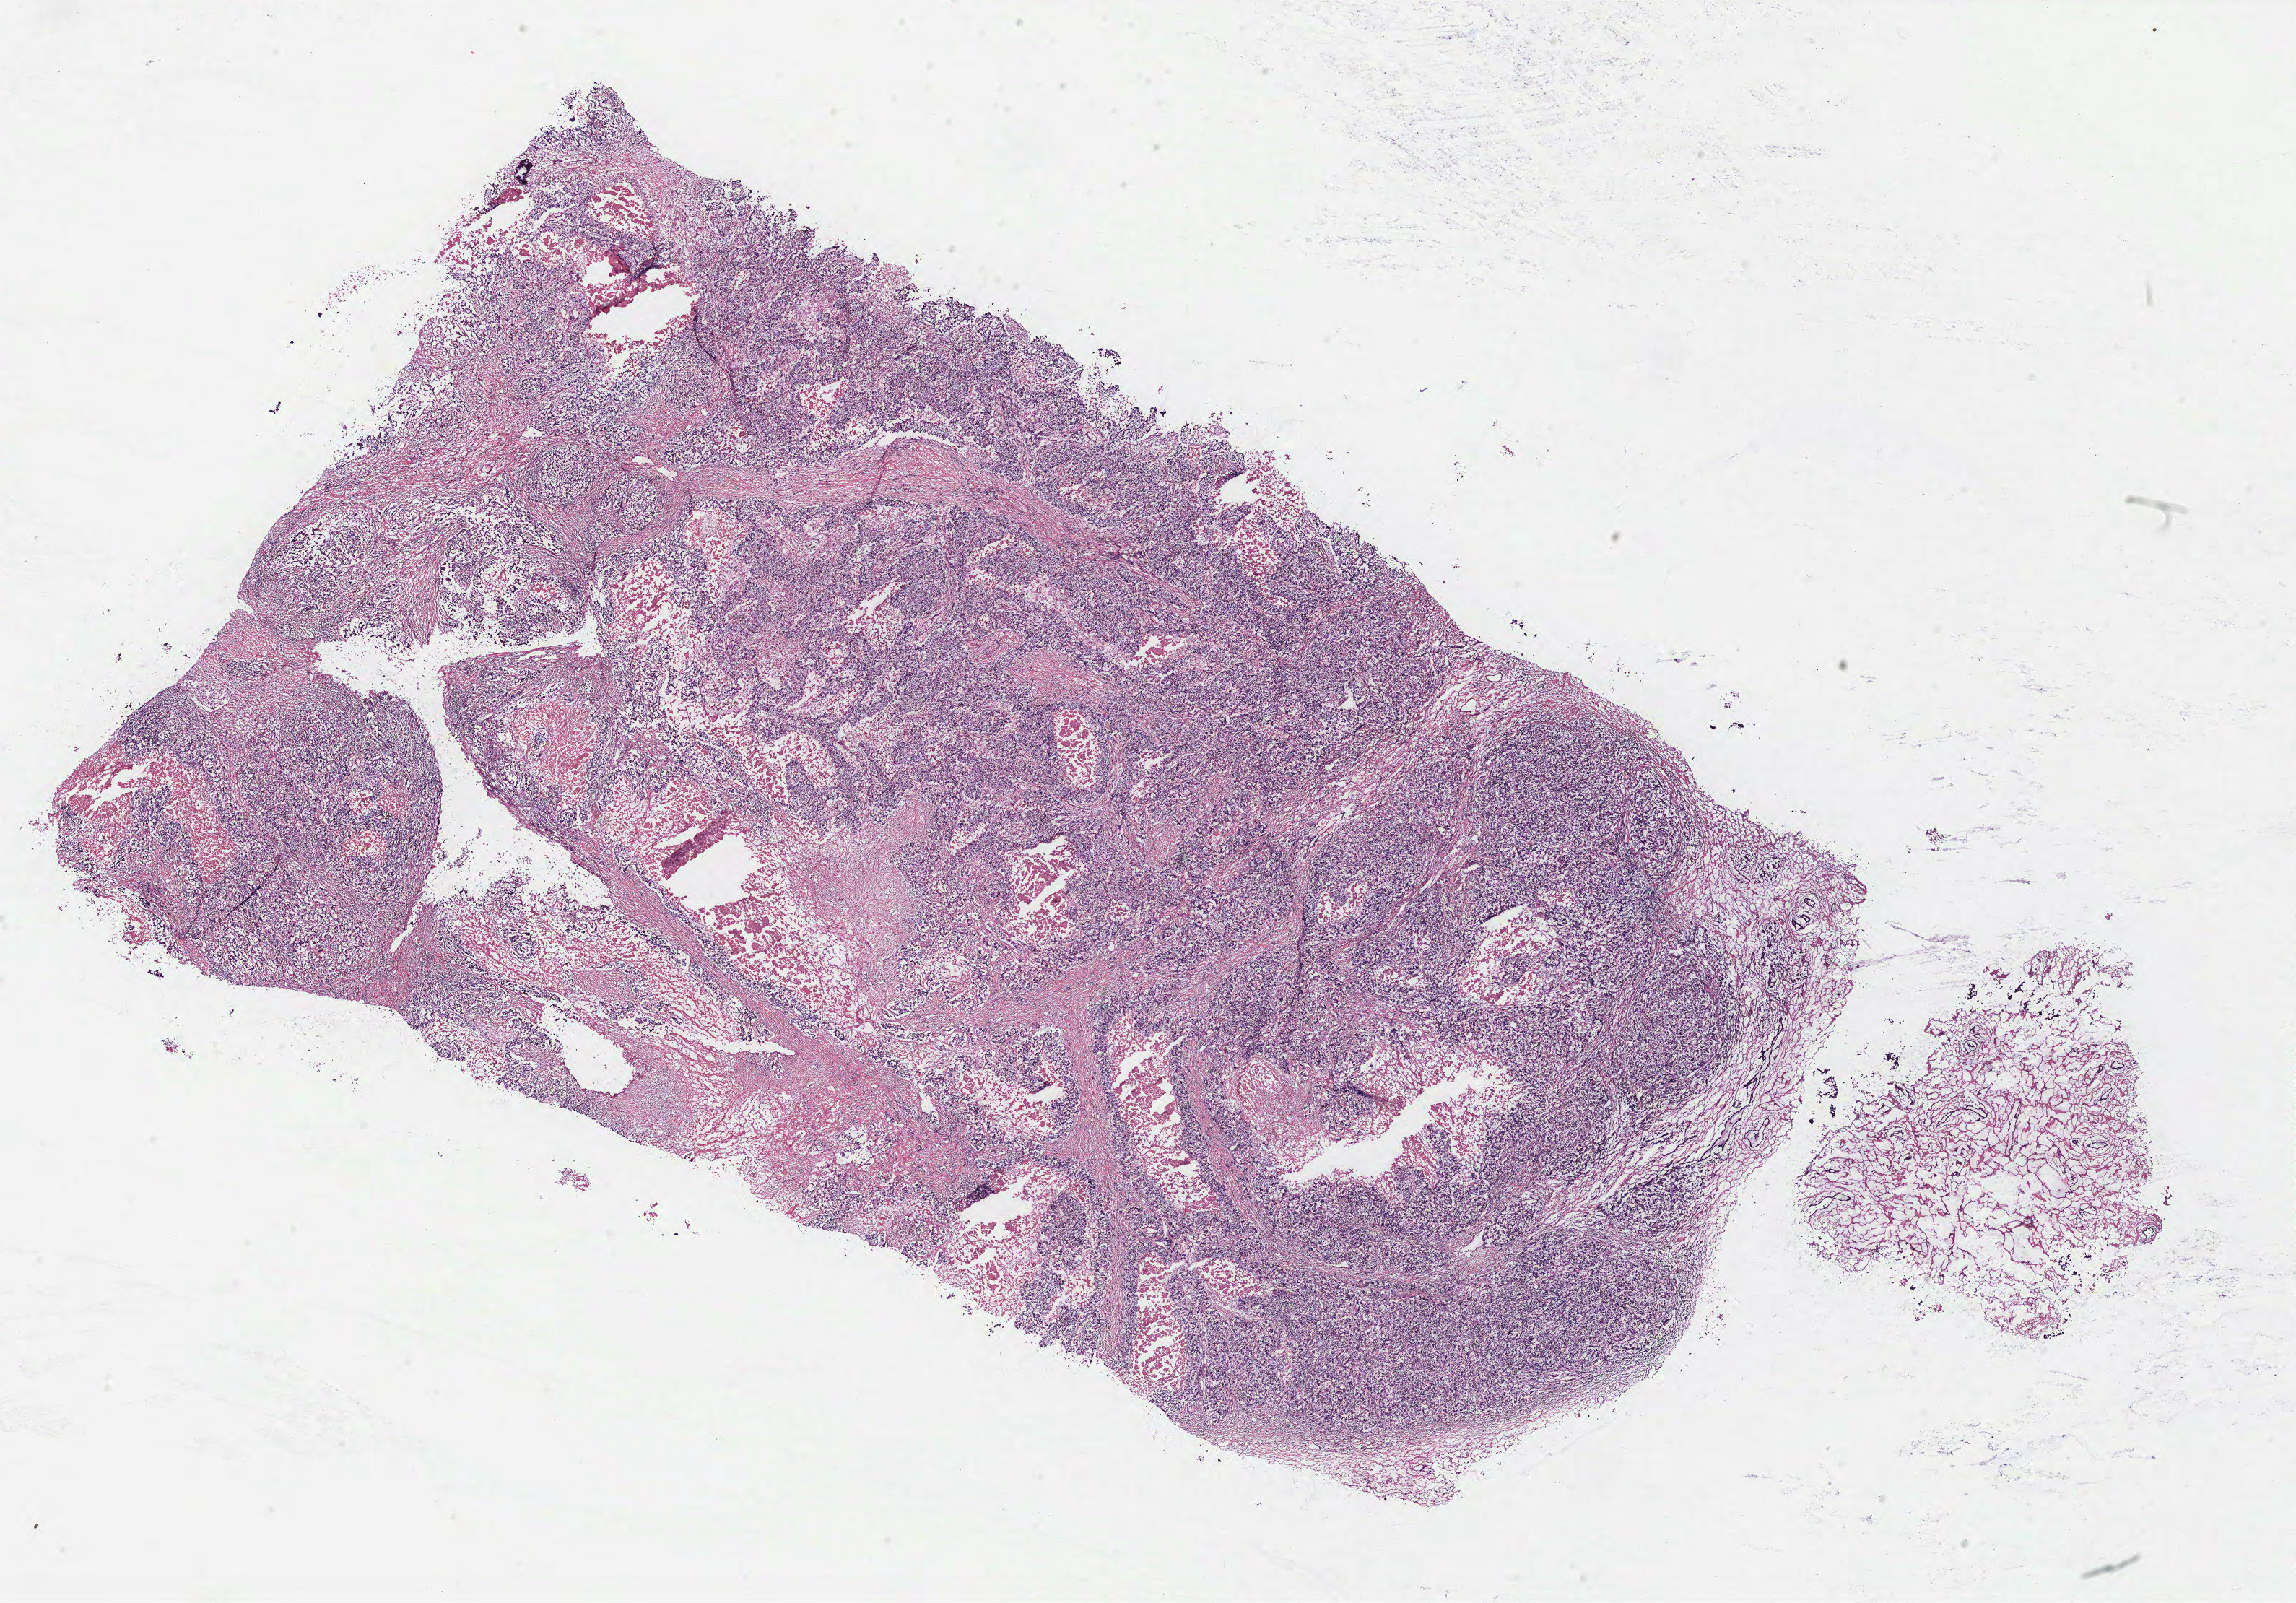
Digitized Hematoxylin and eosin (H&E) stained tissue section (whole slide) — low-resolution overview of the scanned area, about 25.5 x 17.8 mm (slide scanned at 40x), breast, tissue type not recorded. Patient: female, age 75 years.
- patient diagnosis: Infiltrating duct carcinoma, NOS